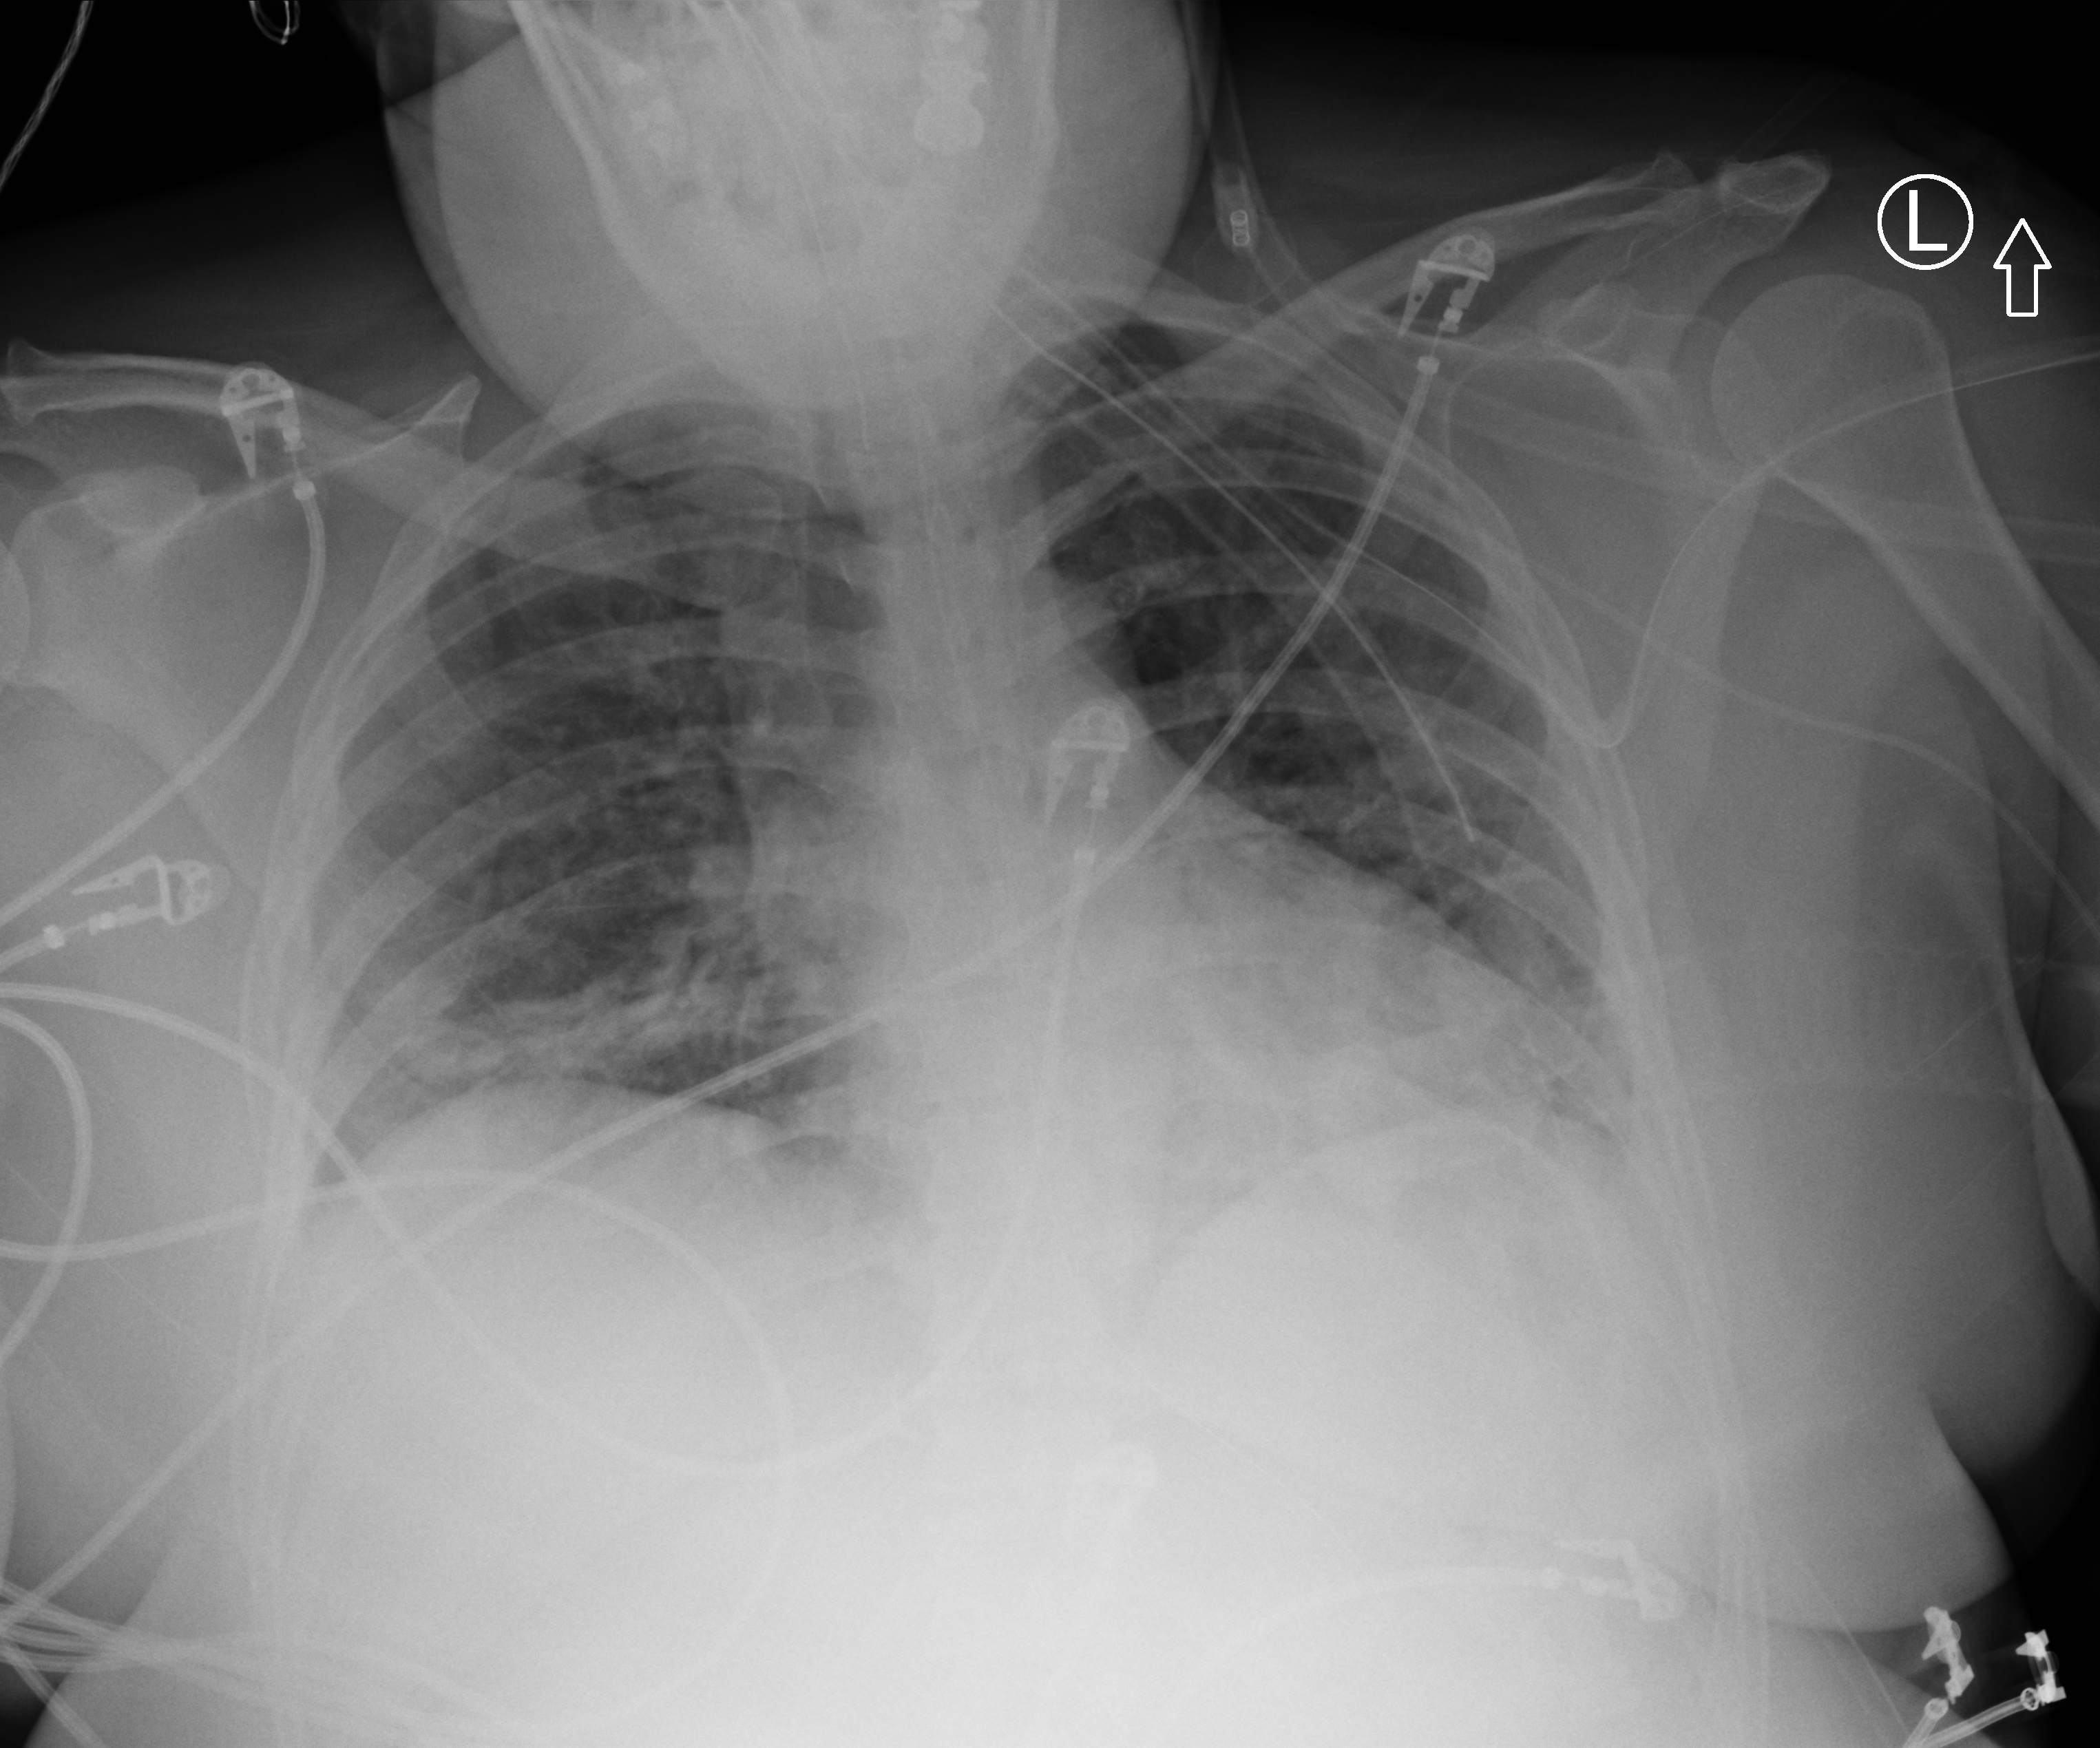
Portable chest radiograph; anteroposterior (AP) projection. Female patient hospitalised with COVID-19, age 18–59 years.
Admission-level facts for this patient (not findings on this image; timing relative to this image not recorded): mechanically ventilated during this hospital stay: yes.